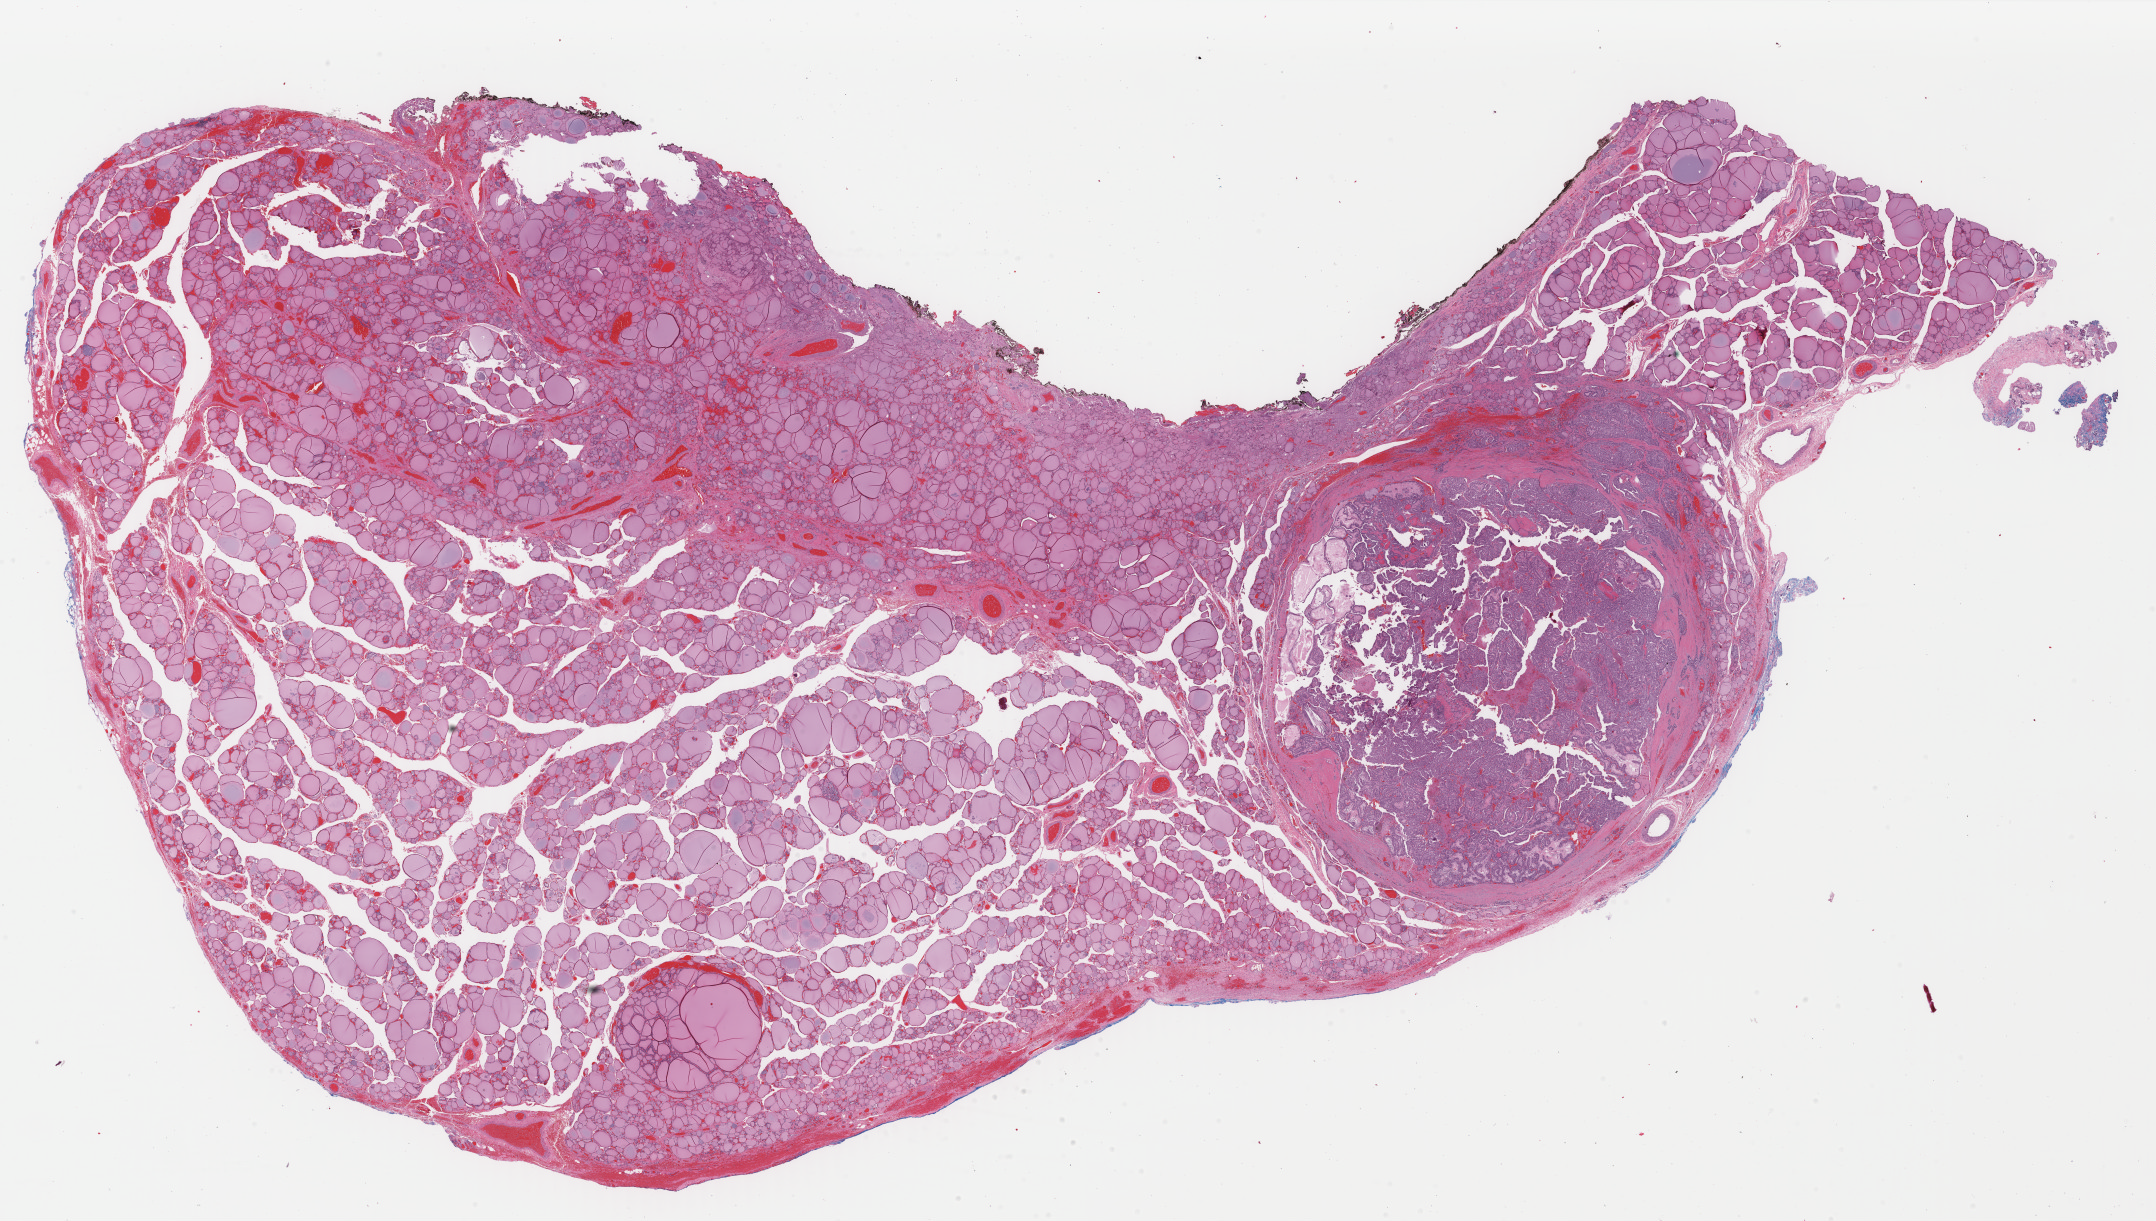
H&E whole-slide image, whole scanned area (about 34.2 x 19.4 mm, from a 40x scan) shown as a low-resolution overview. FFPE section. Primary tumour sample from the thyroid. Patient: female, age at initial diagnosis 47 years.
TNM: T1a N0 M0. Laterality: left. AJCC pathologic stage: I. Diagnosis: Papillary carcinoma, columnar cell. Lymph nodes positive (case pathology): 0 of 3 examined.